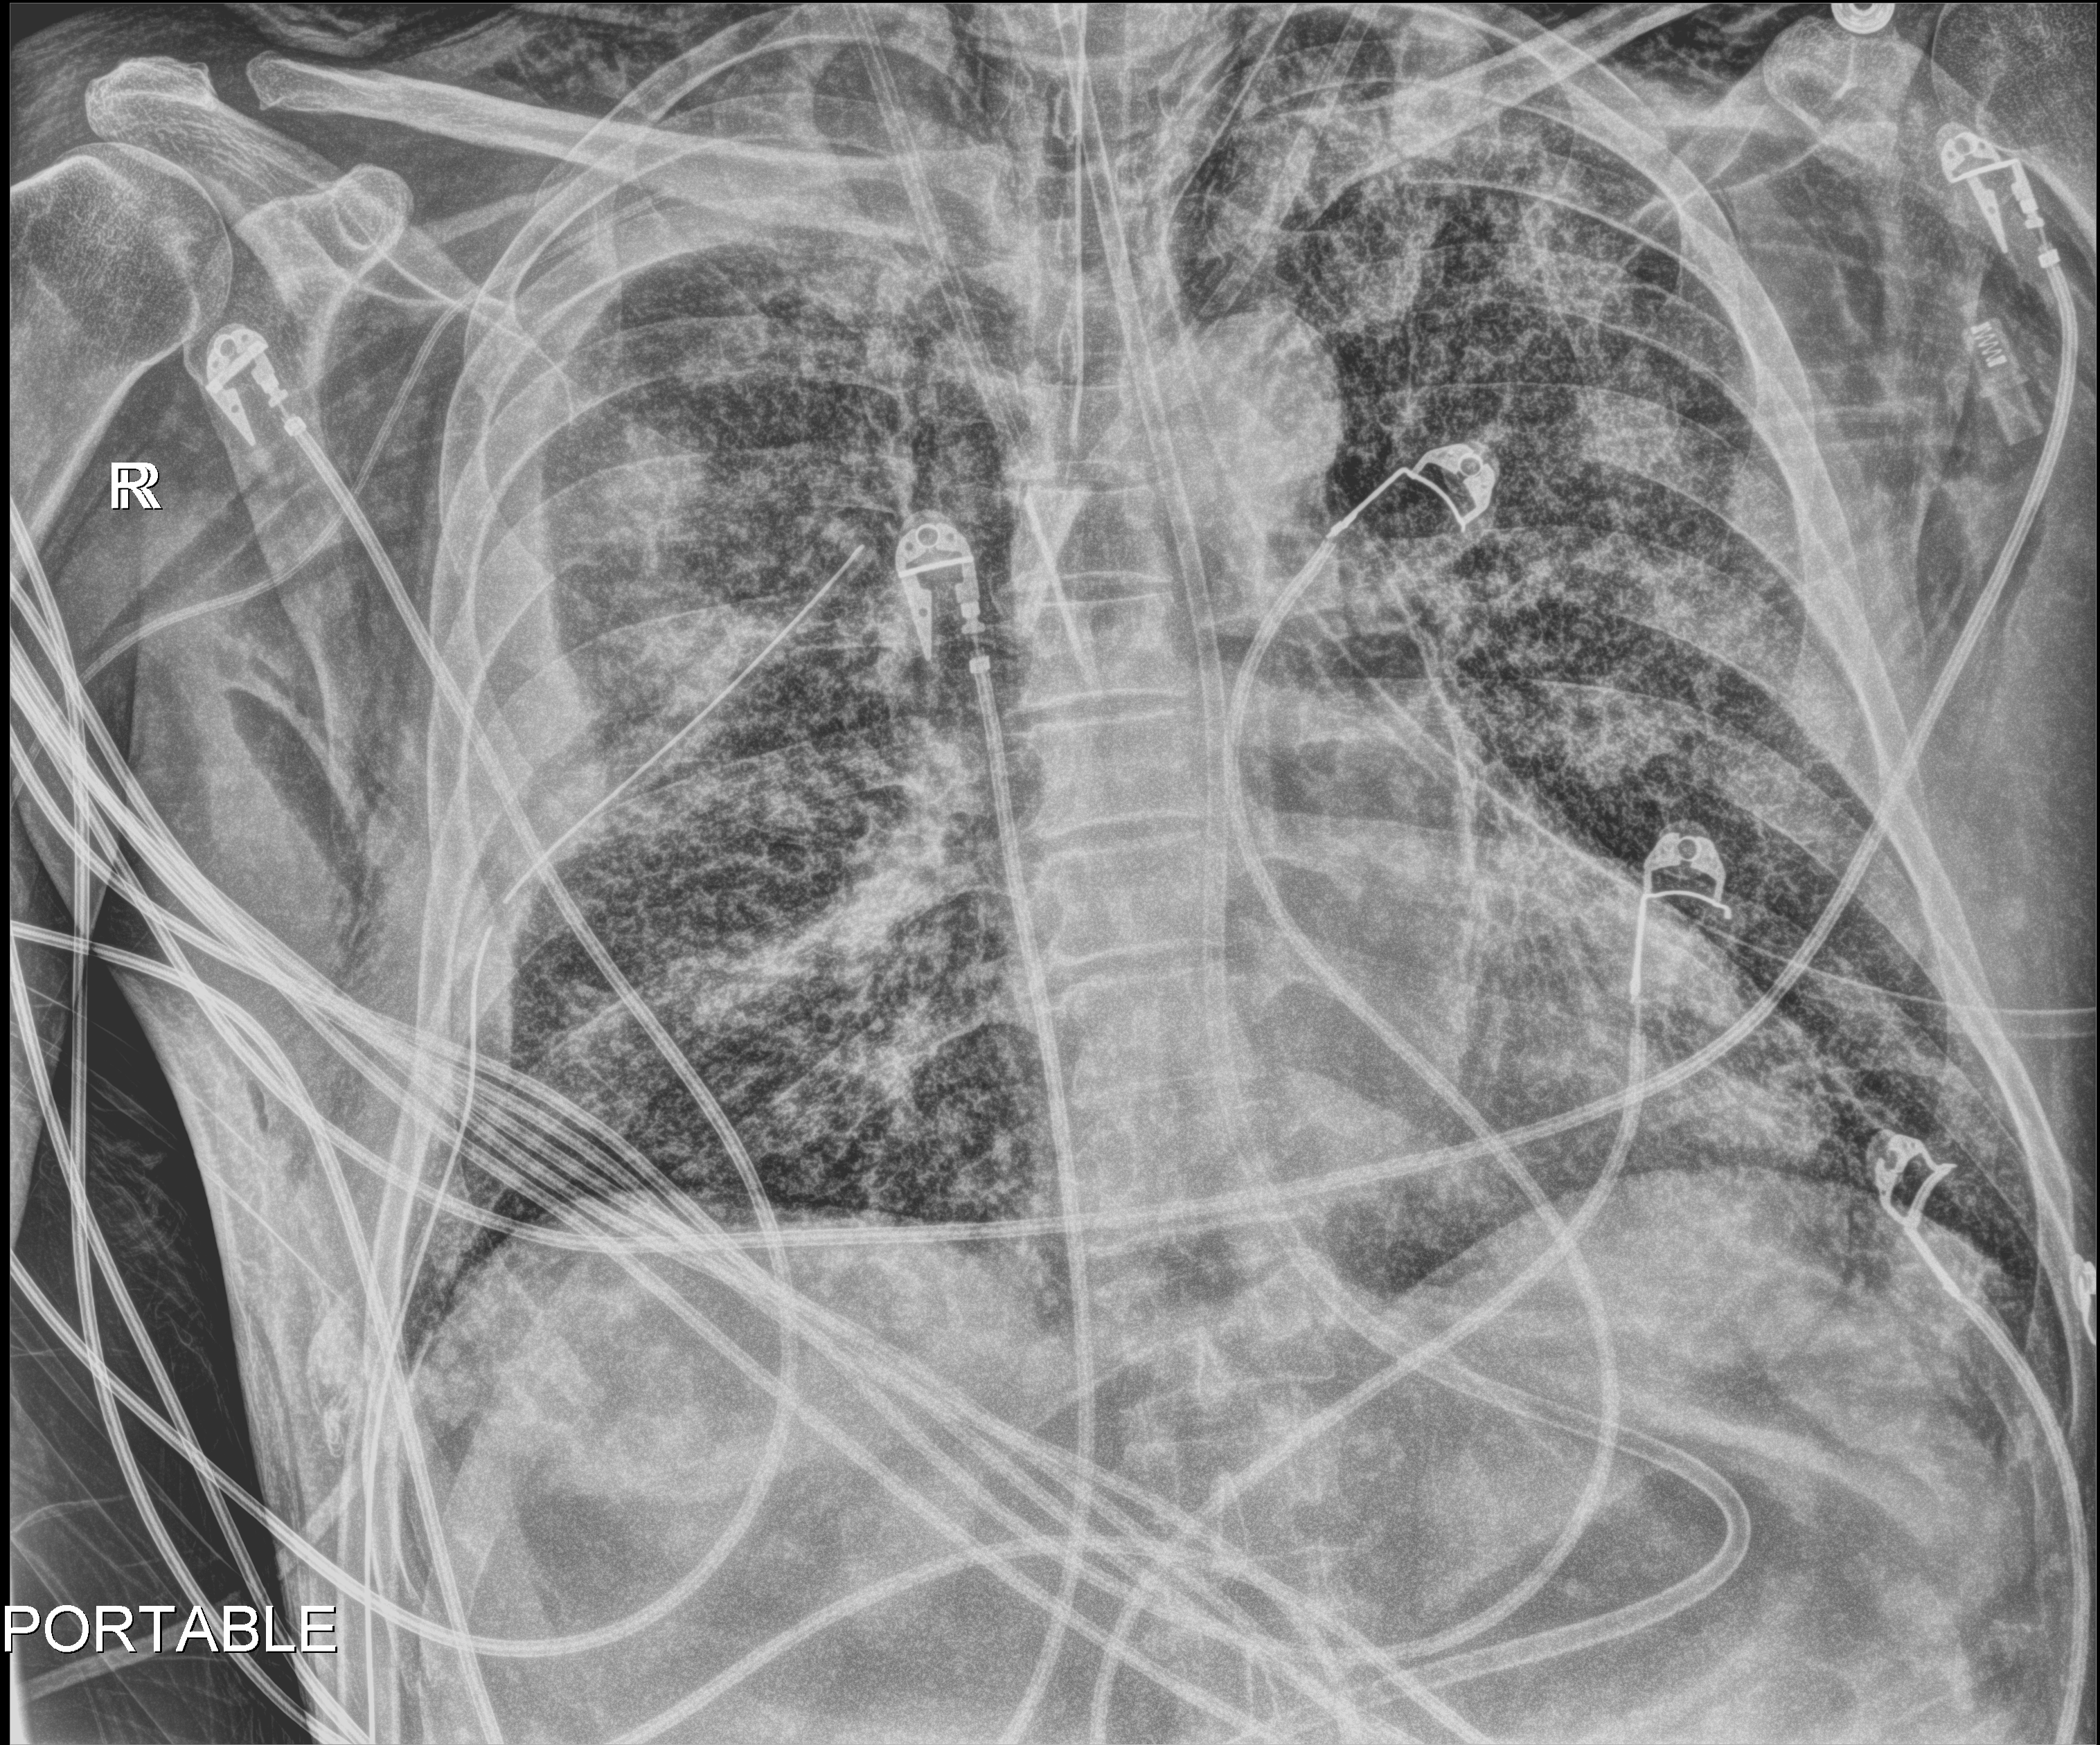
Bedside chest radiograph (digital radiography), anteroposterior (AP) projection. Patient hospitalised with COVID-19; male, aged 18–59 years.
Admission-level facts for this patient (not findings on this image; timing relative to this image not recorded): mechanically ventilated during this hospital stay: yes; smoking status (admission record): never; admitted to intensive care during this hospital stay: yes.